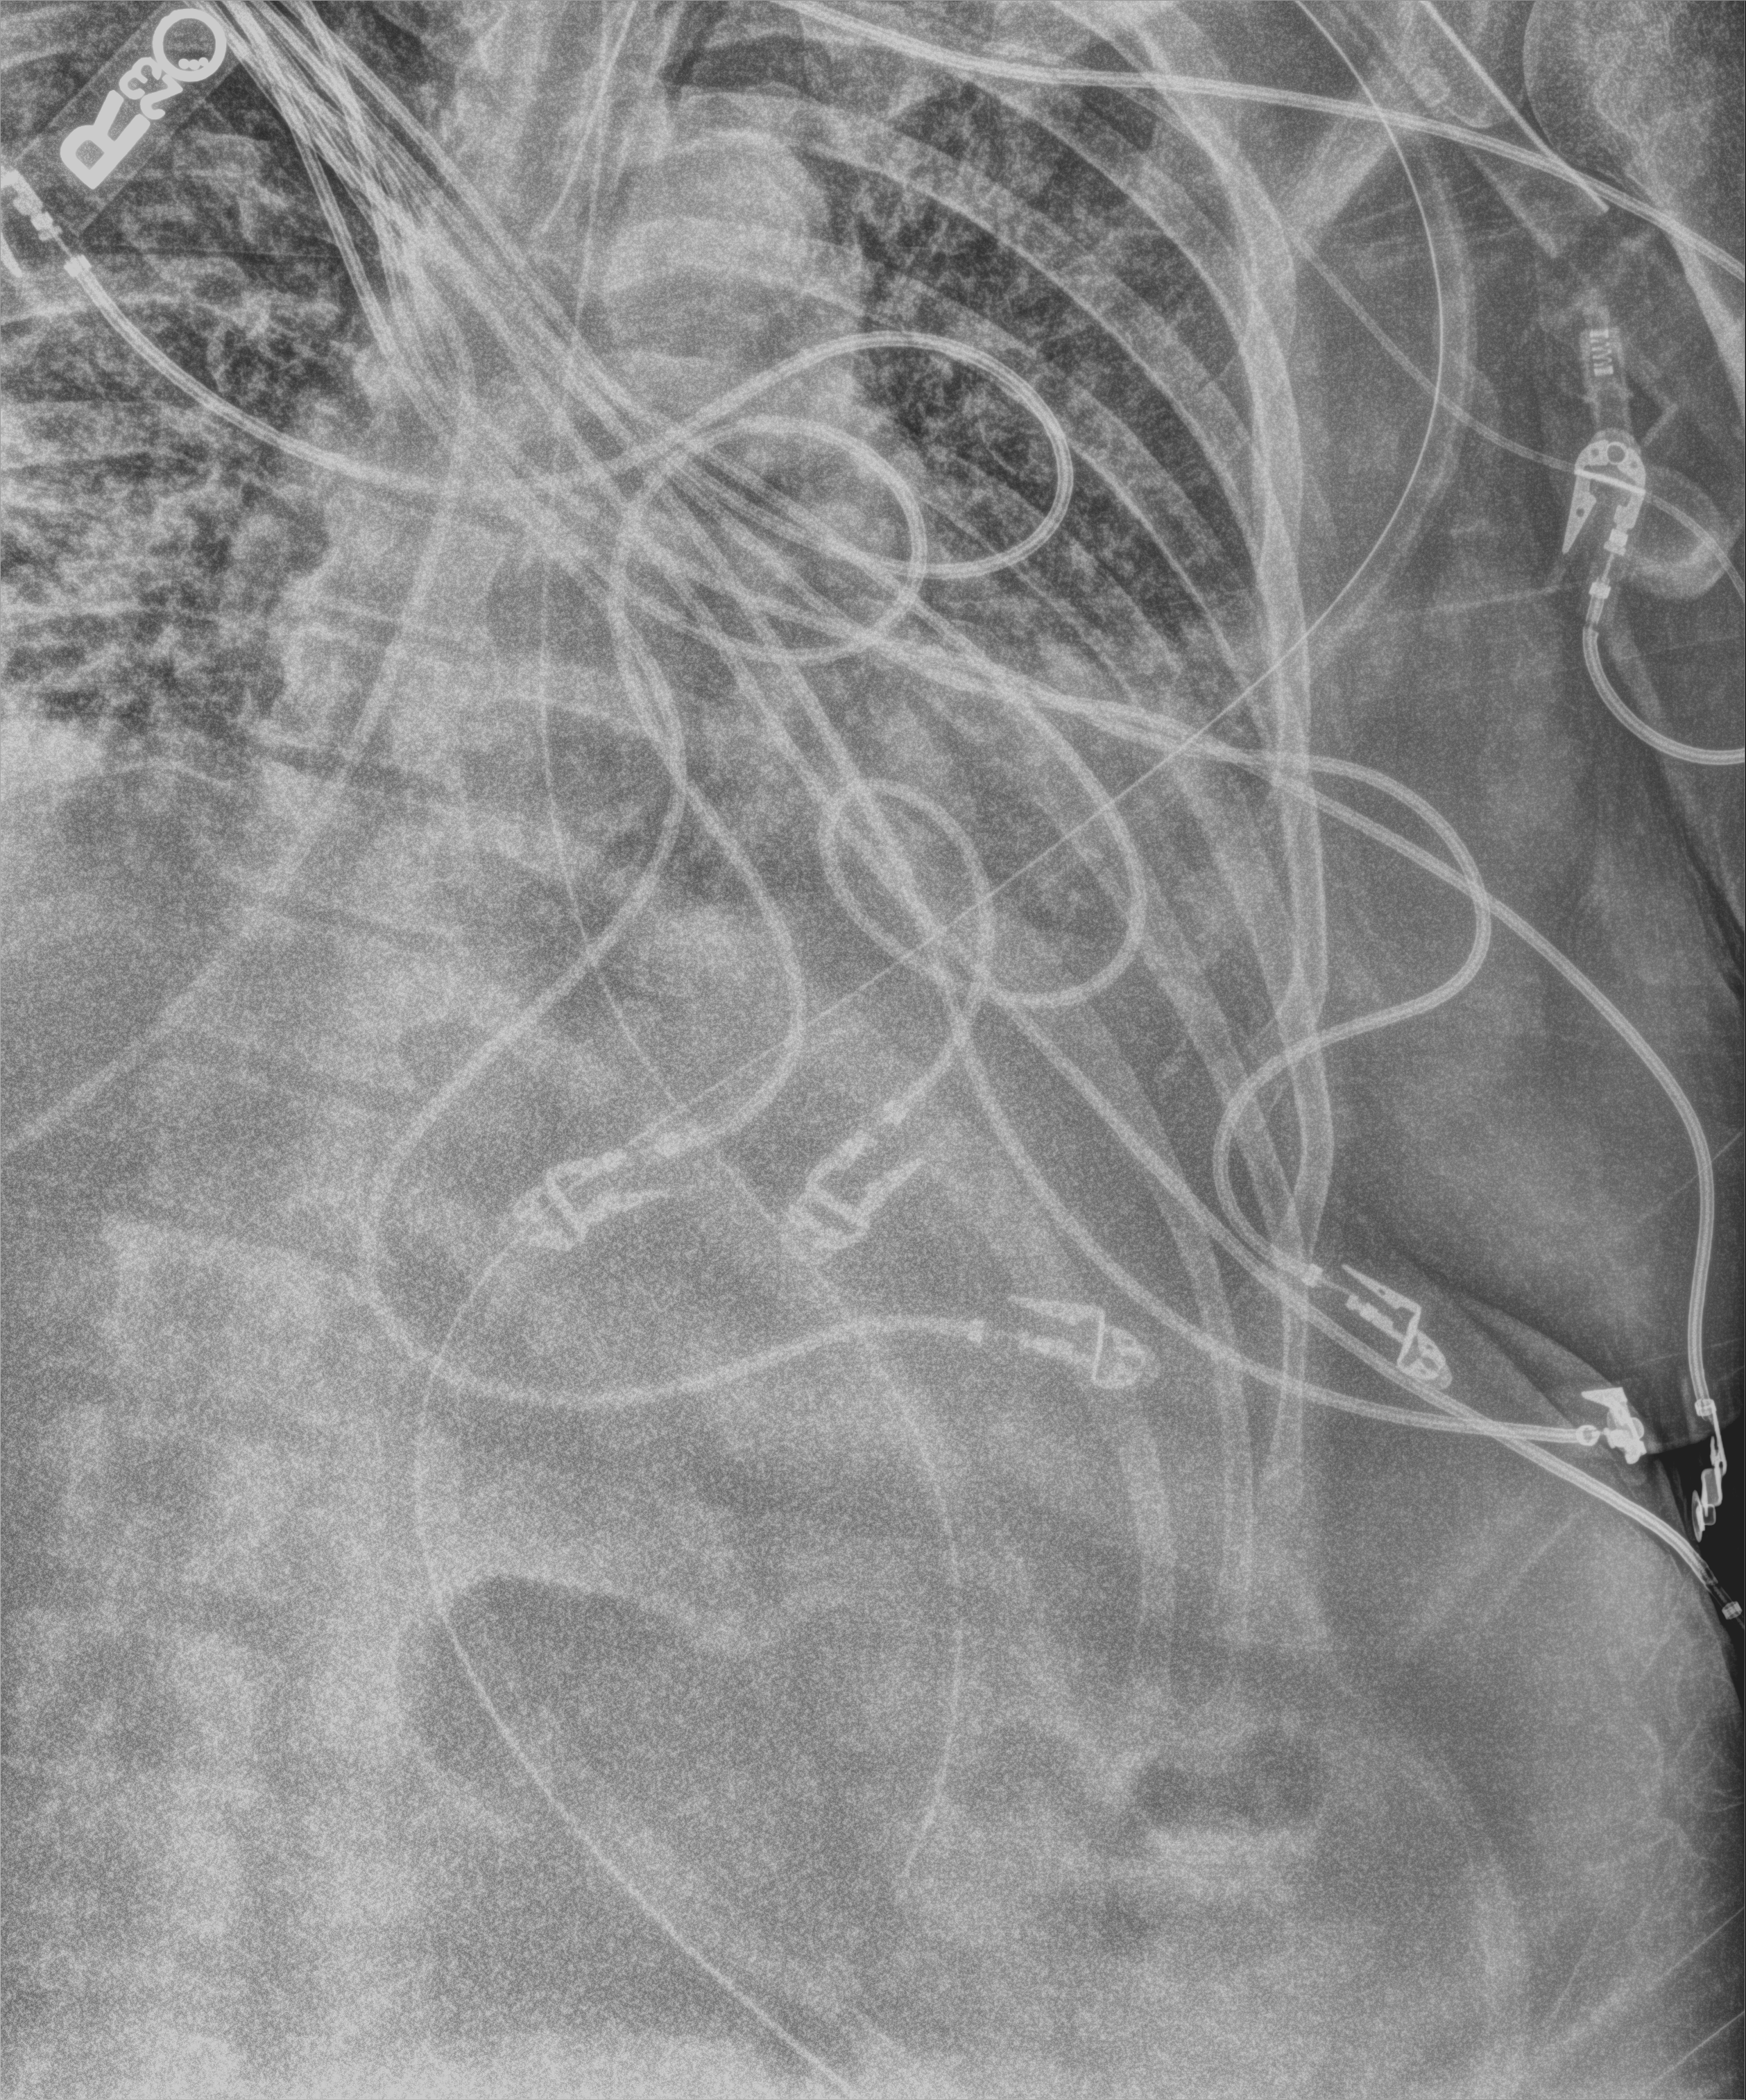
Chest X-ray (portable), anteroposterior (AP) projection. Patient hospitalised with COVID-19; male, aged 60–74 years.
Hospital-stay facts (about this admission, not read from this image; timing relative to this image not recorded): admitted to intensive care during this hospital stay: yes; other chronic lung disease (admission record): no; hypertension (admission record): yes.